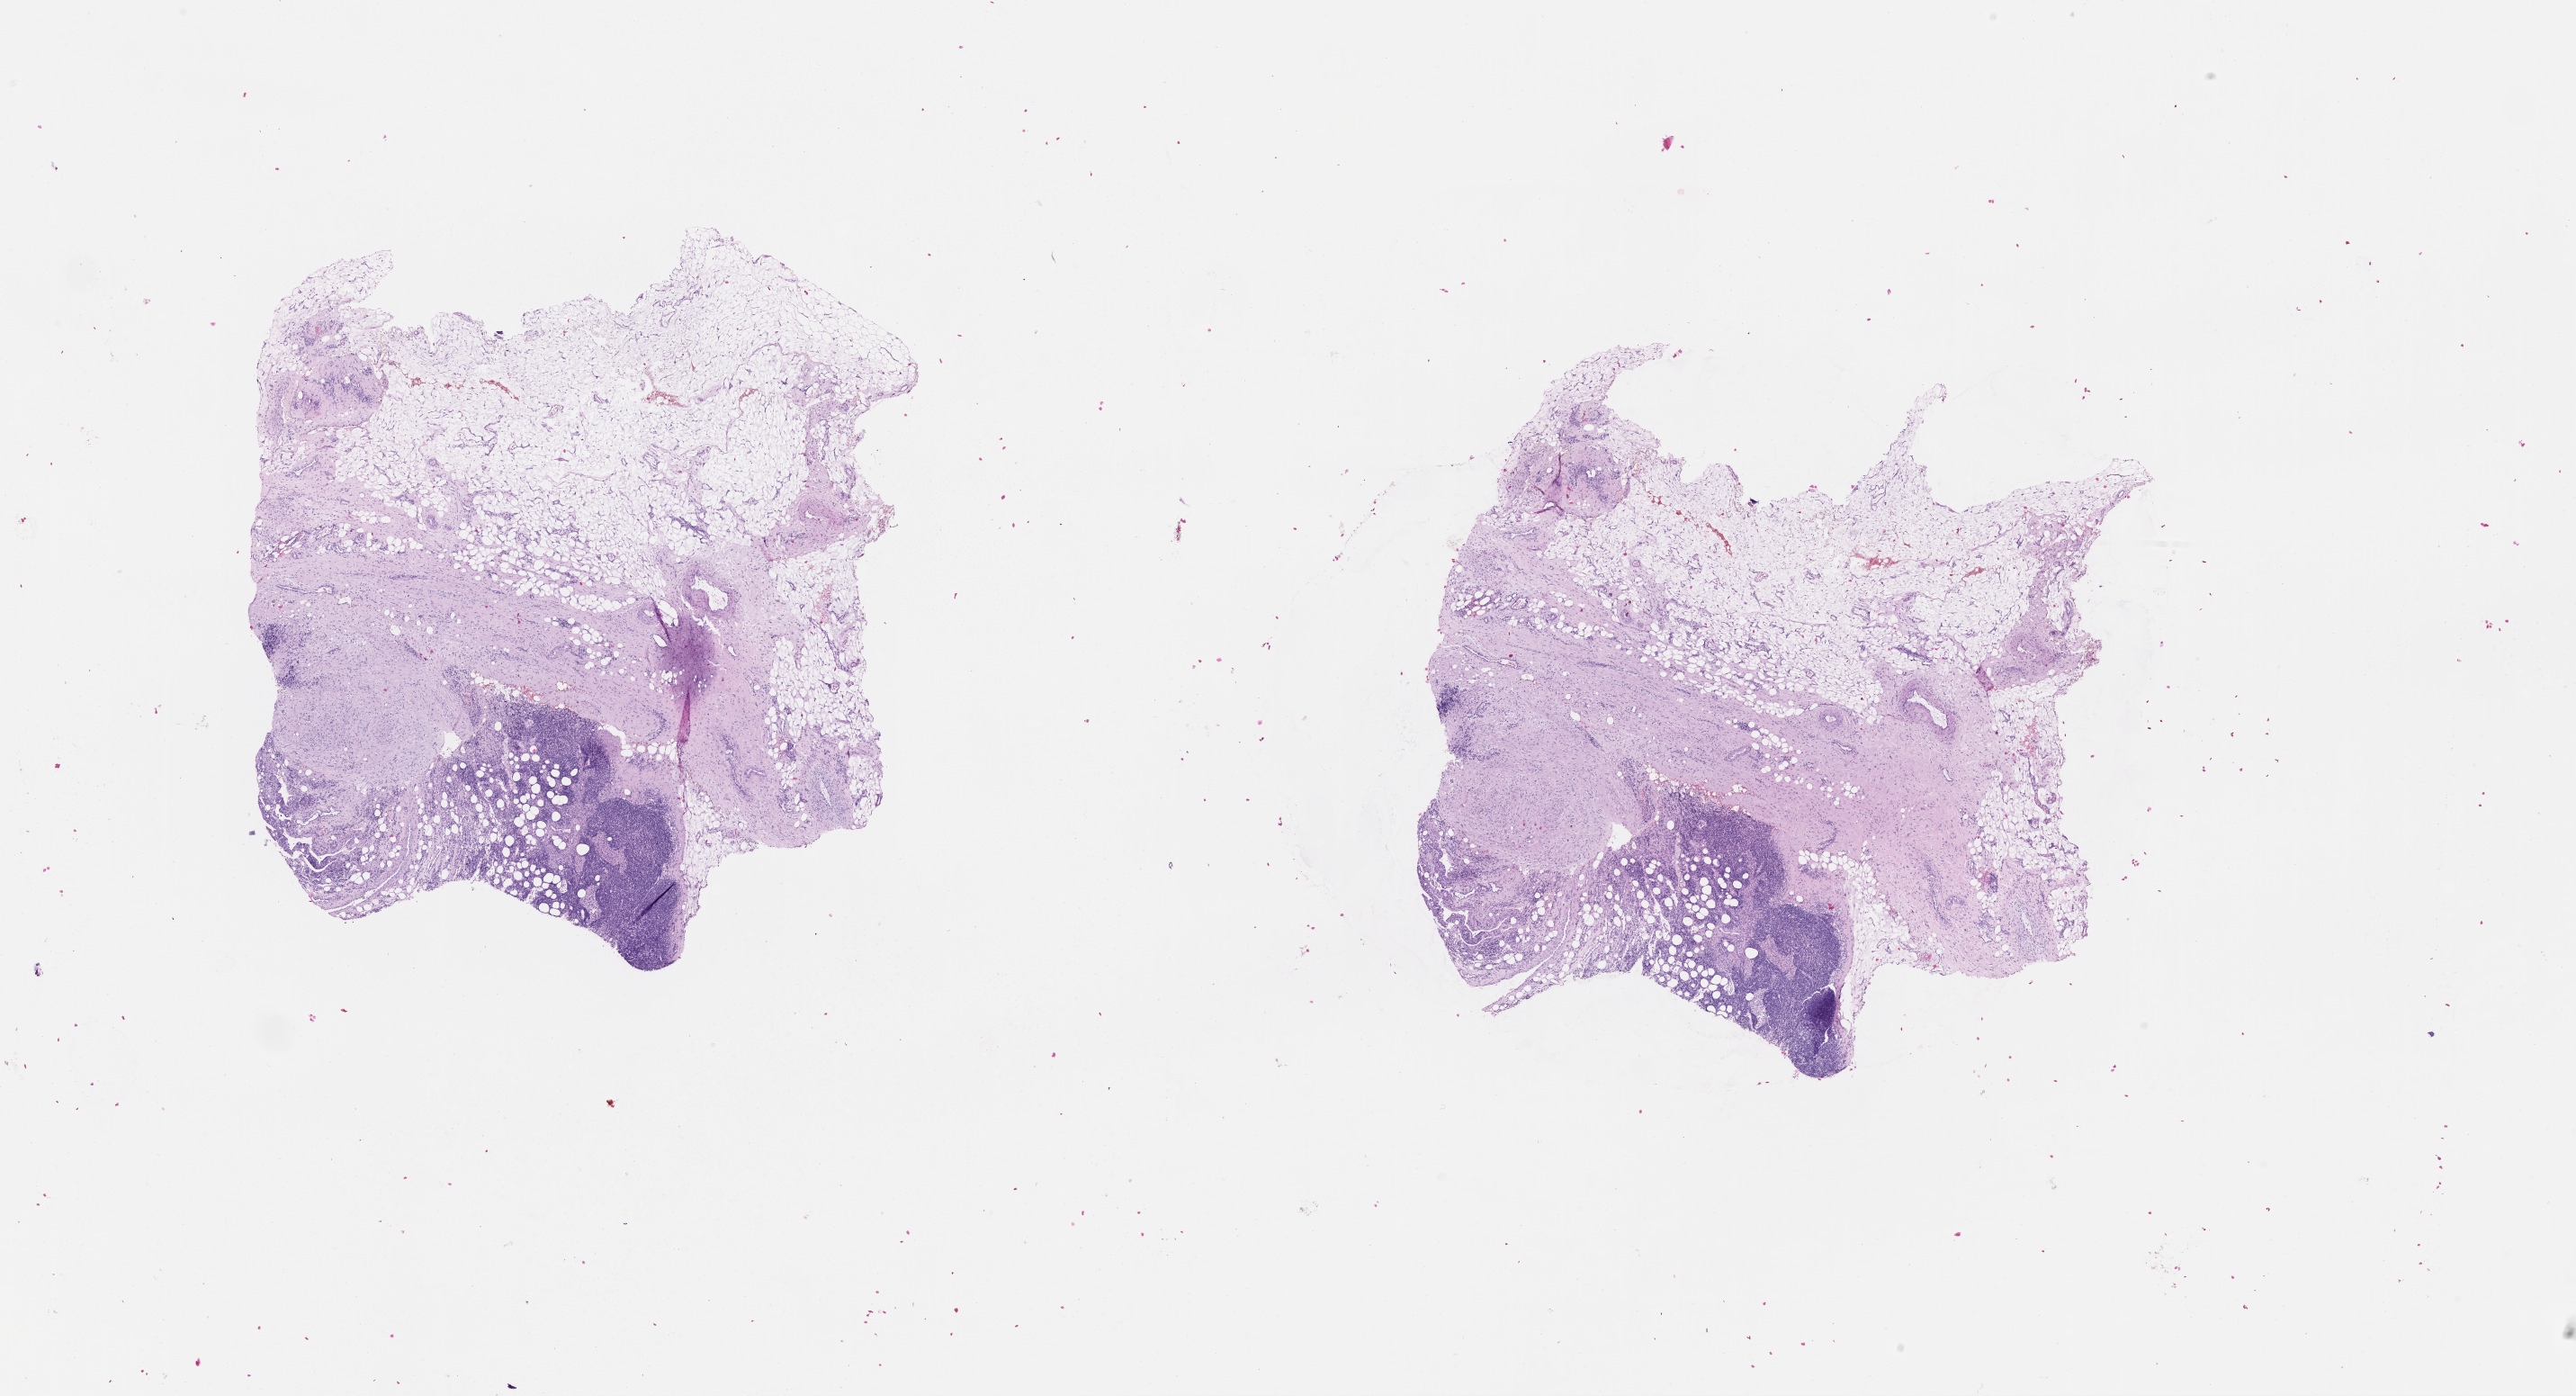
Whole-slide histology image, H&E, shown as a low-resolution overview of the whole scanned area (about 23.1 x 12.5 mm, slide scanned at 20x). Male, 72 y/o.
- patient diagnosis: Malignant melanoma, NOS